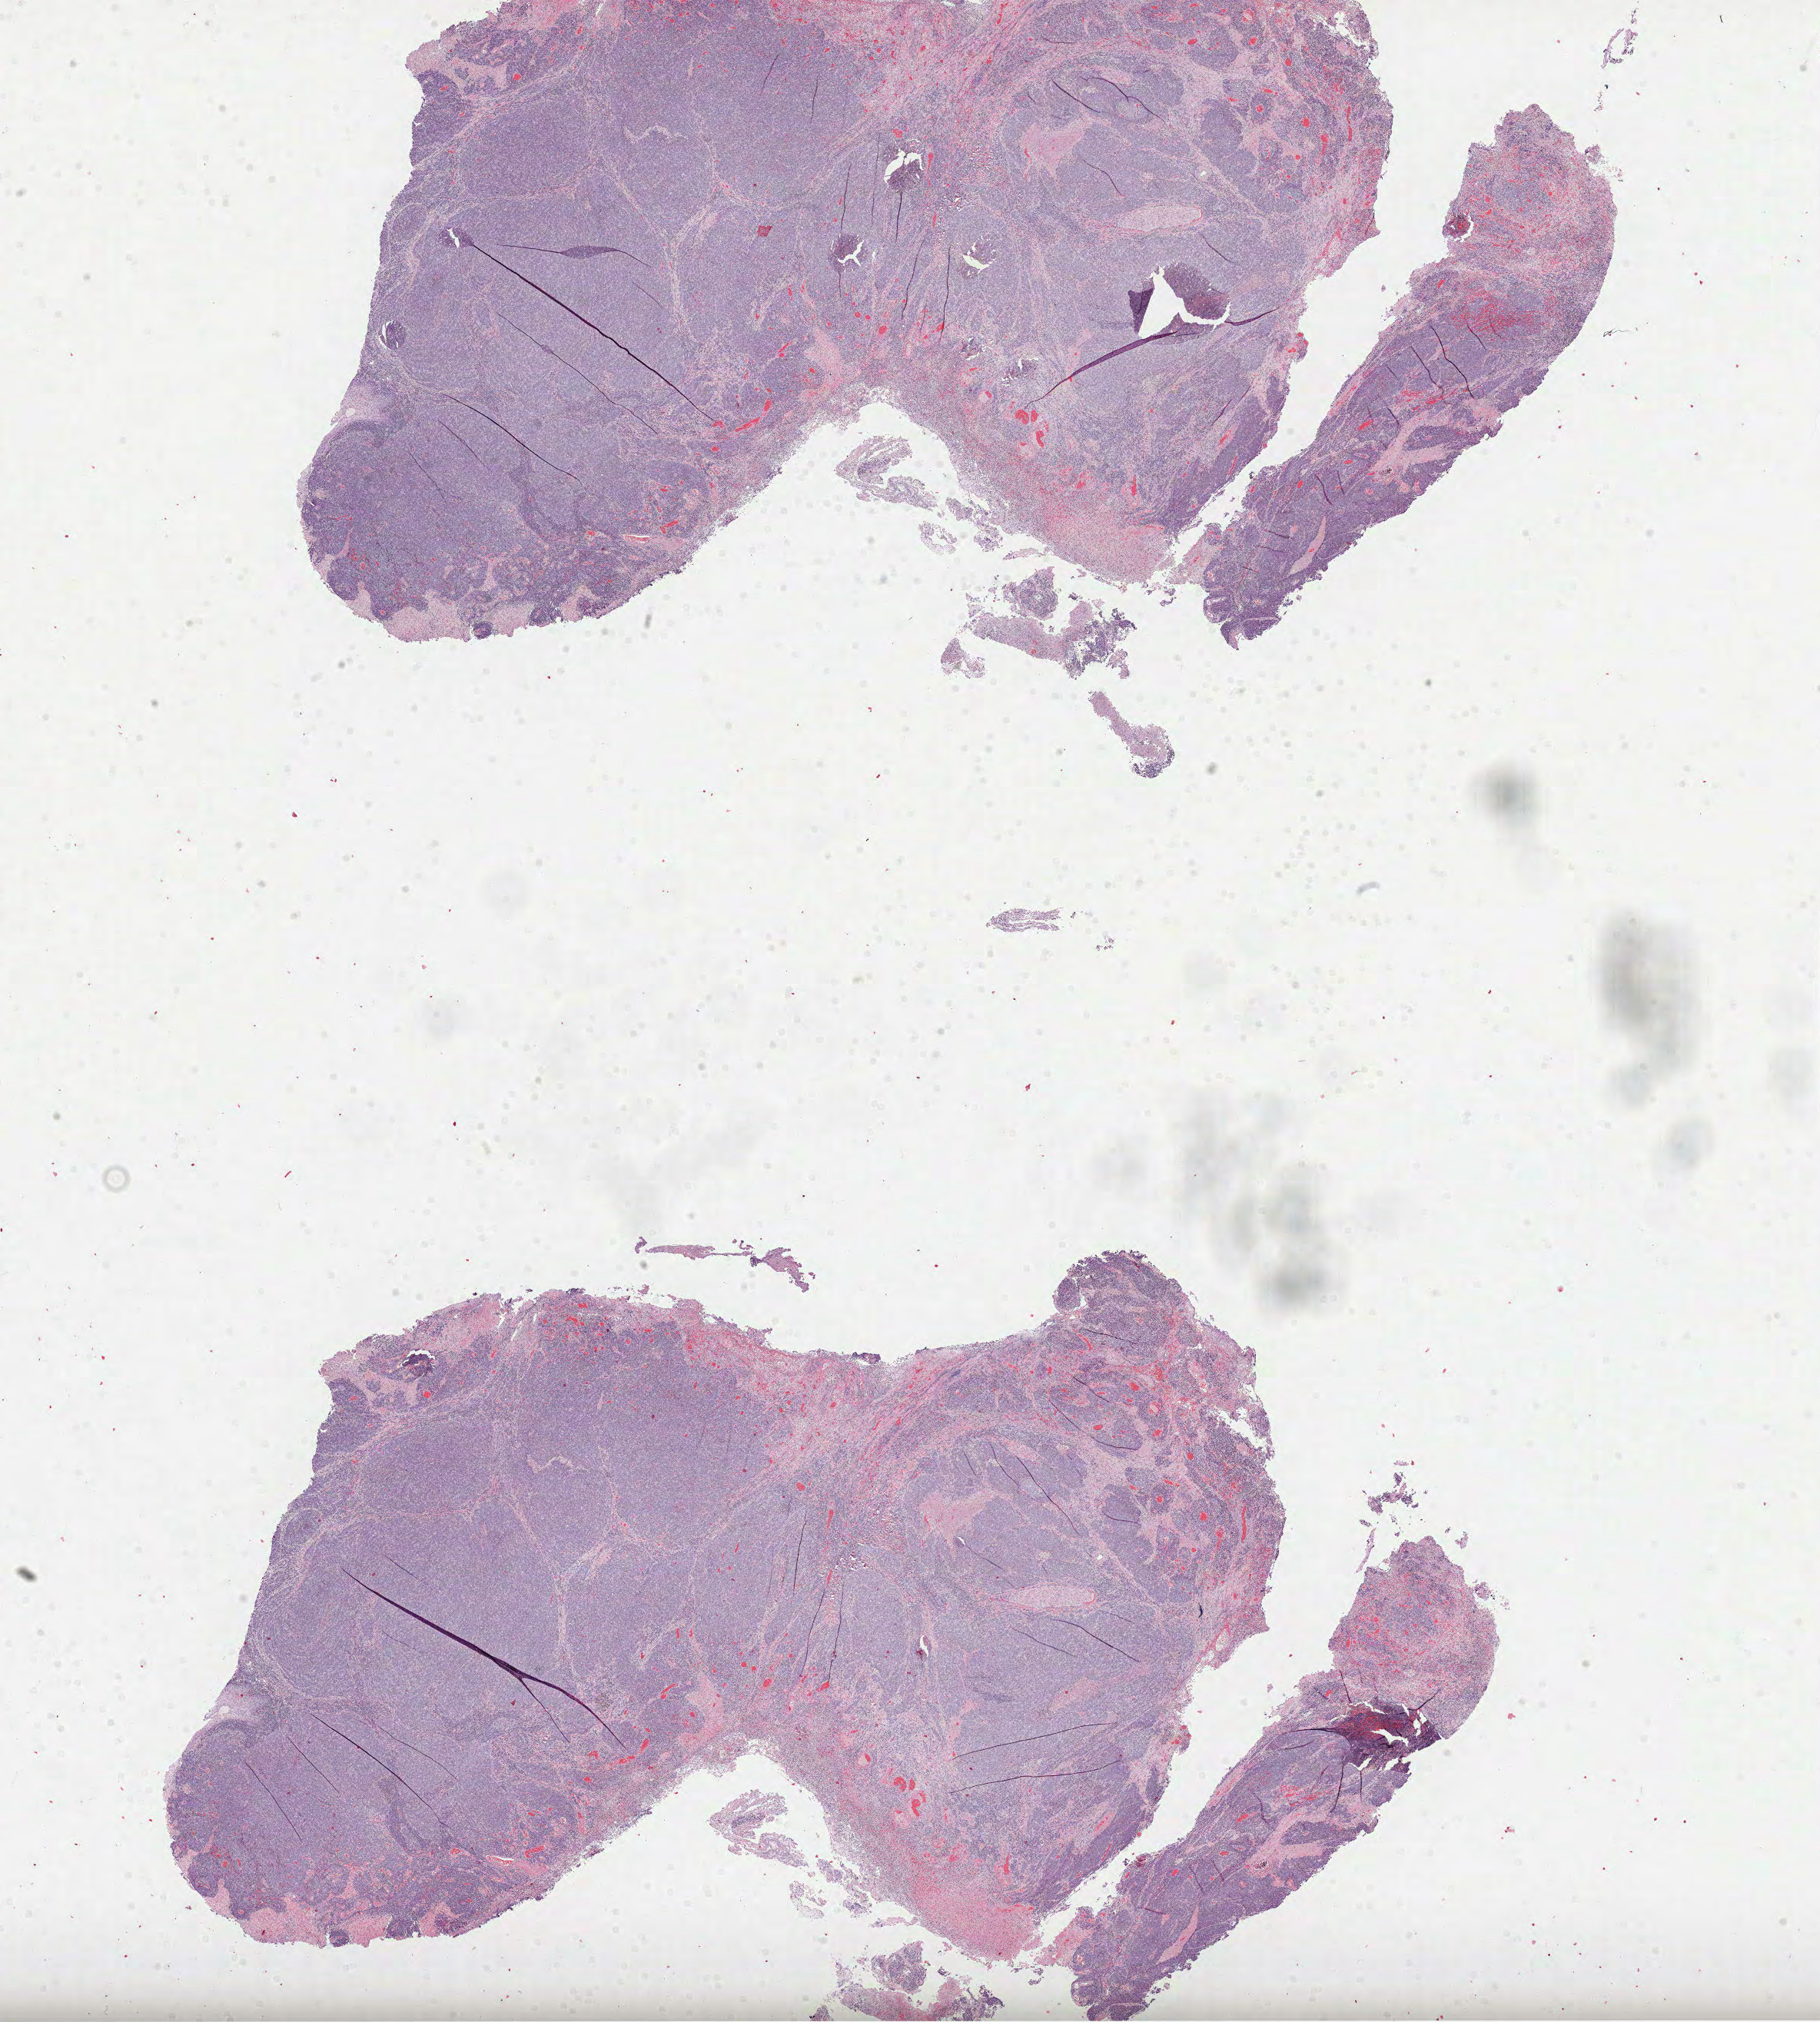
Whole-slide histology image, H&E-stained — whole scanned area (about 19.1 x 21.2 mm) shown as a low-resolution overview, formalin-fixed paraffin-embedded (FFPE) diagnostic section, sample: primary tumour, head and neck. Male patient; age at initial diagnosis 52 years. Histologic grade: G3 (poorly differentiated).
Laterality: left. AJCC pathologic stage: IVA (7th edition). Histologic diagnosis: Squamous cell carcinoma, NOS (larynx, NOS).